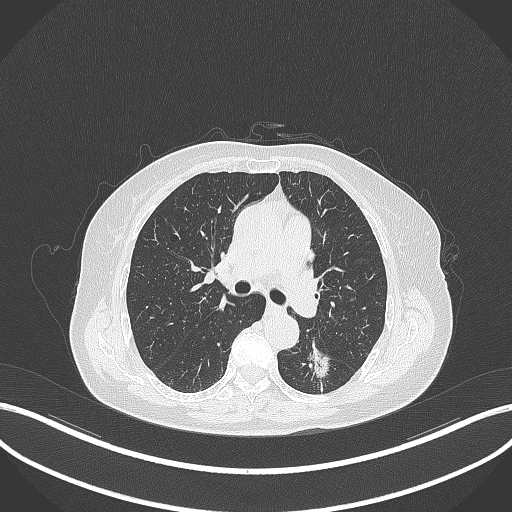
Chest CT, one axial slice; position 180 of 352 along the scan axis; reconstruction kernel B70f; 120 kVp; lung window (W 1500 / L -600 HU); 1 mm slice thickness; 512 × 512 image matrix. Female patient, age 70 years. Case-level facts recorded for this patient, not image findings: clinical TNM (as recorded): T1c N0 M0.
Outlined on this slice (rectangle marked by the reading radiologist):
- lung tumour (recorded histology: adenocarcinoma): bounding box (x1, y1, x2, y2) in pixels: (296, 328, 337, 387)